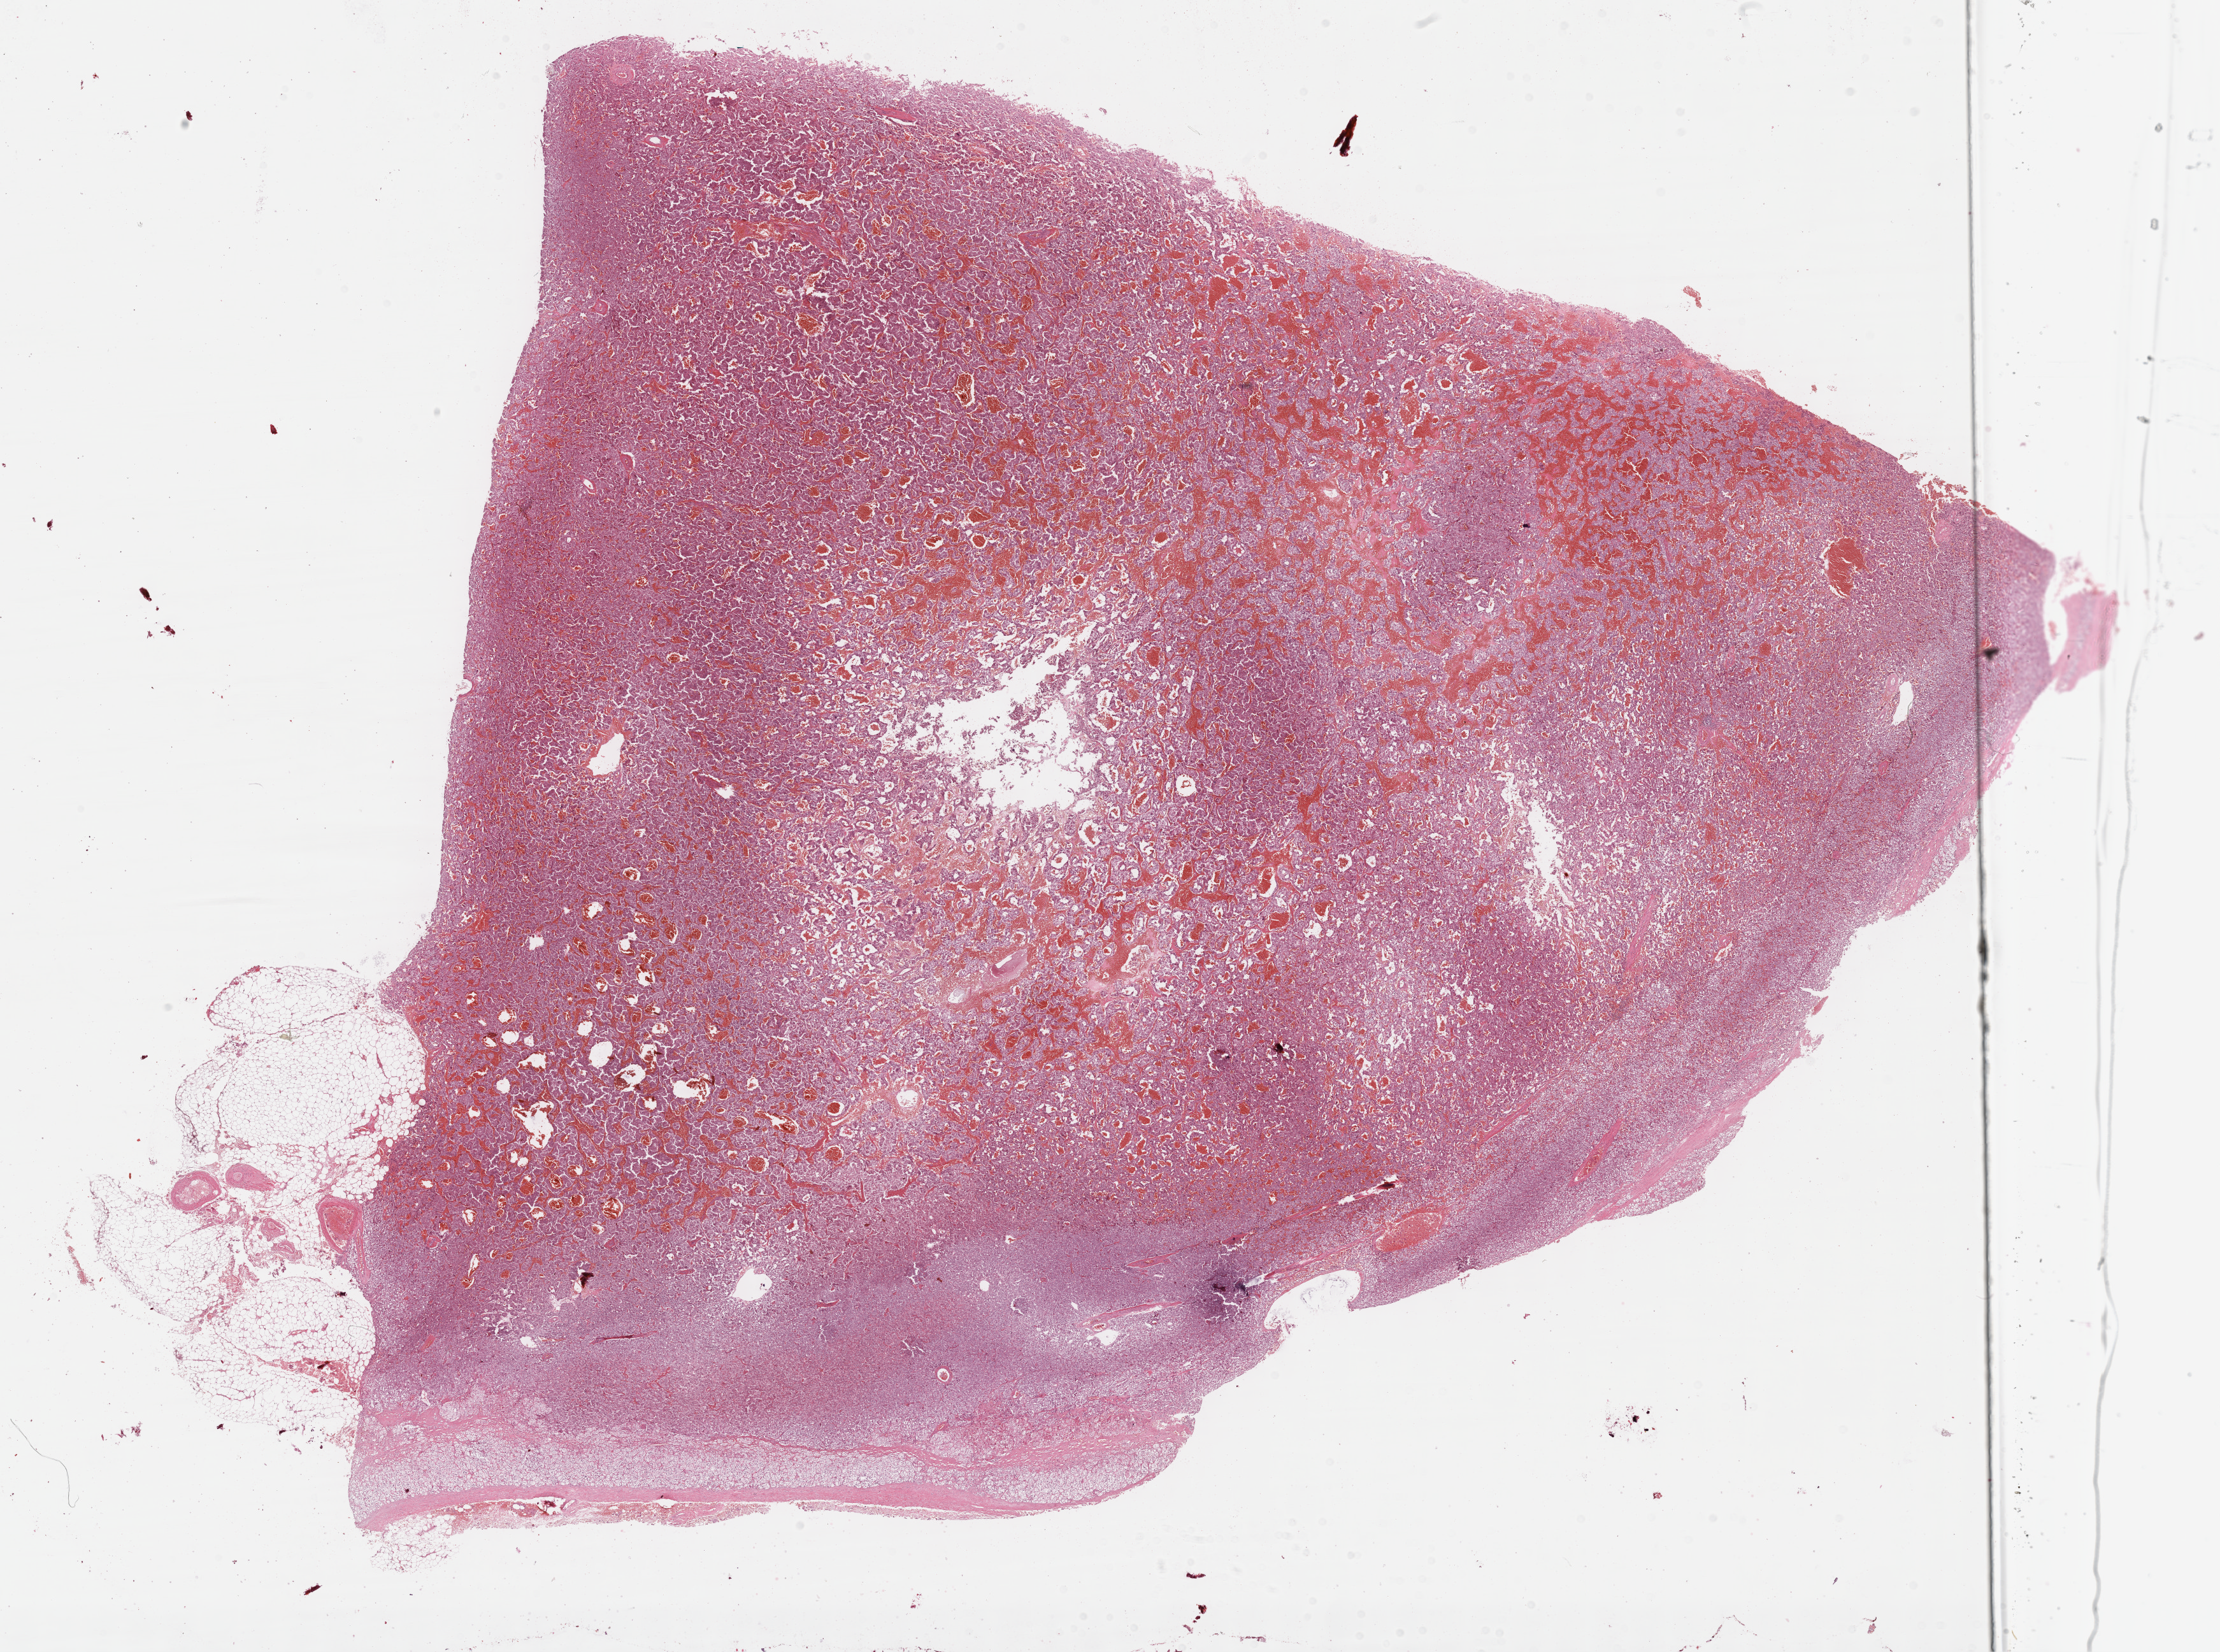
Whole-slide histology image, H&E — low-resolution overview of the scanned area, about 28.2 x 21.0 mm. Formalin-fixed paraffin-embedded (FFPE) diagnostic section. Primary tumour sample from the adrenal gland. Patient: male, age at initial diagnosis 52 years.
Histologic diagnosis: Pheochromocytoma, malignant.